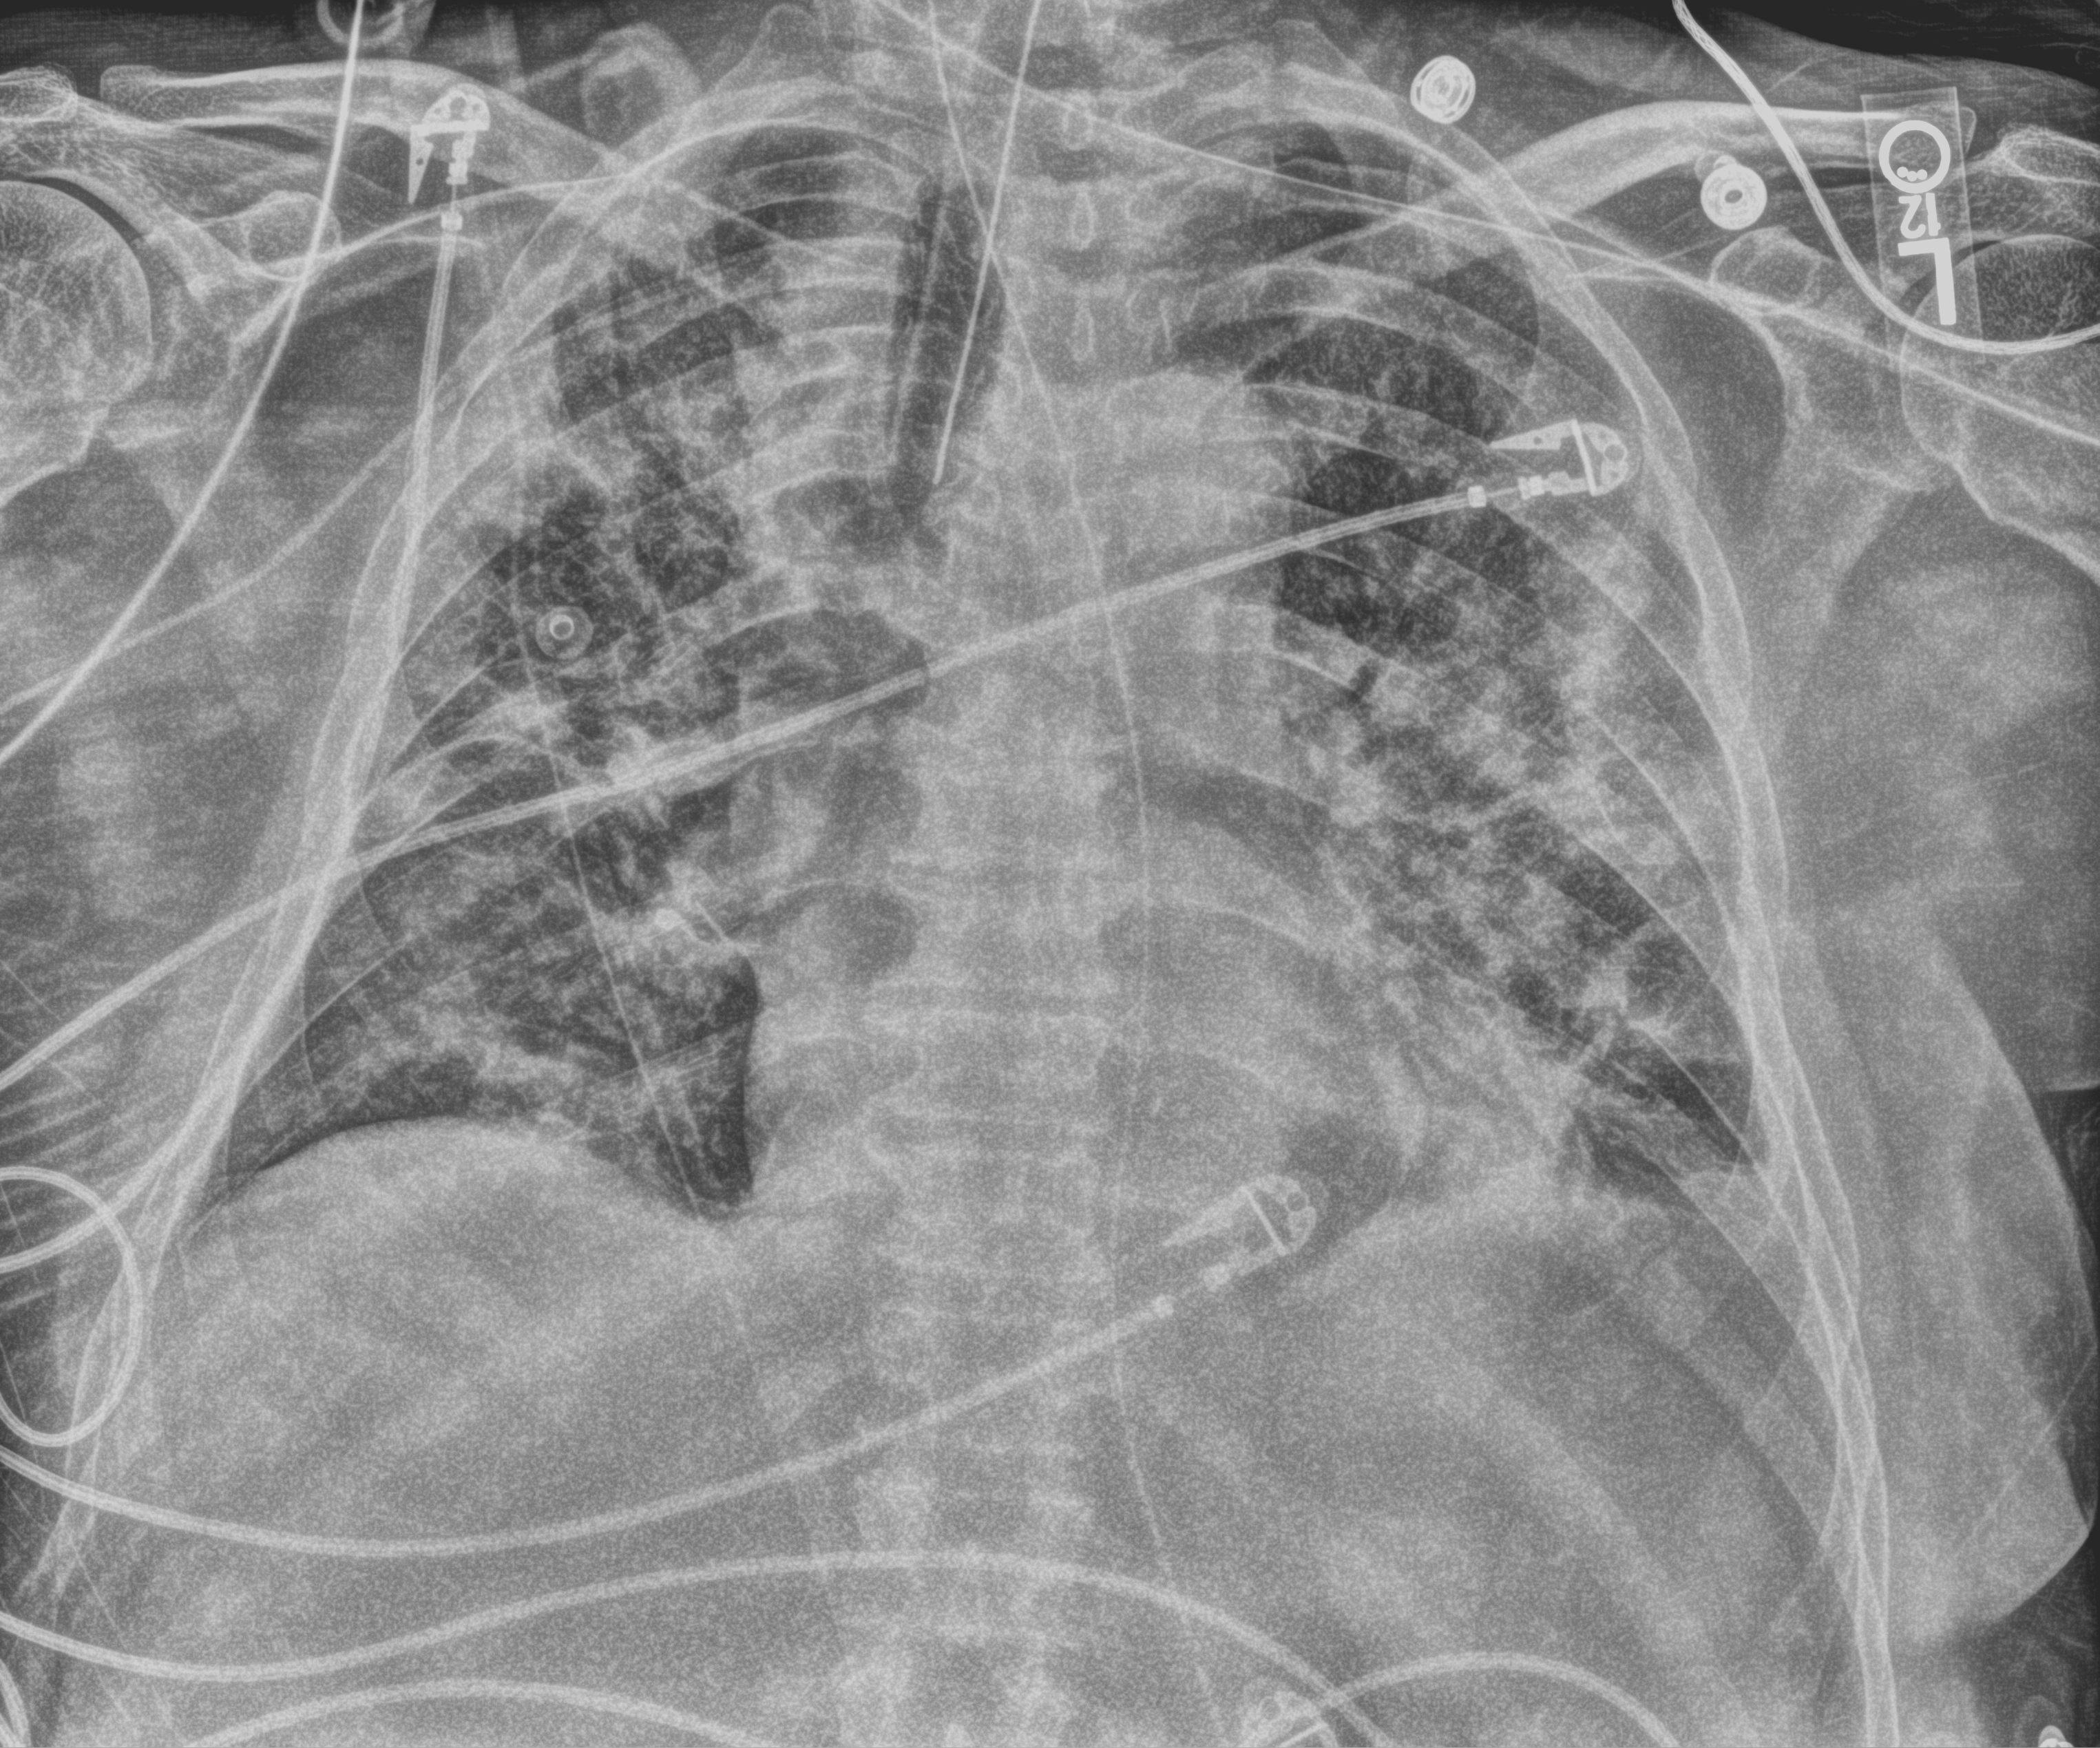
Bedside chest radiograph (computed radiography); anteroposterior (AP) projection. Male patient hospitalised with COVID-19, age 60–74 years.
Hospital-stay facts (about this admission, not read from this image; timing relative to this image not recorded): admitted to intensive care during this hospital stay: yes; mechanically ventilated during this hospital stay: yes.